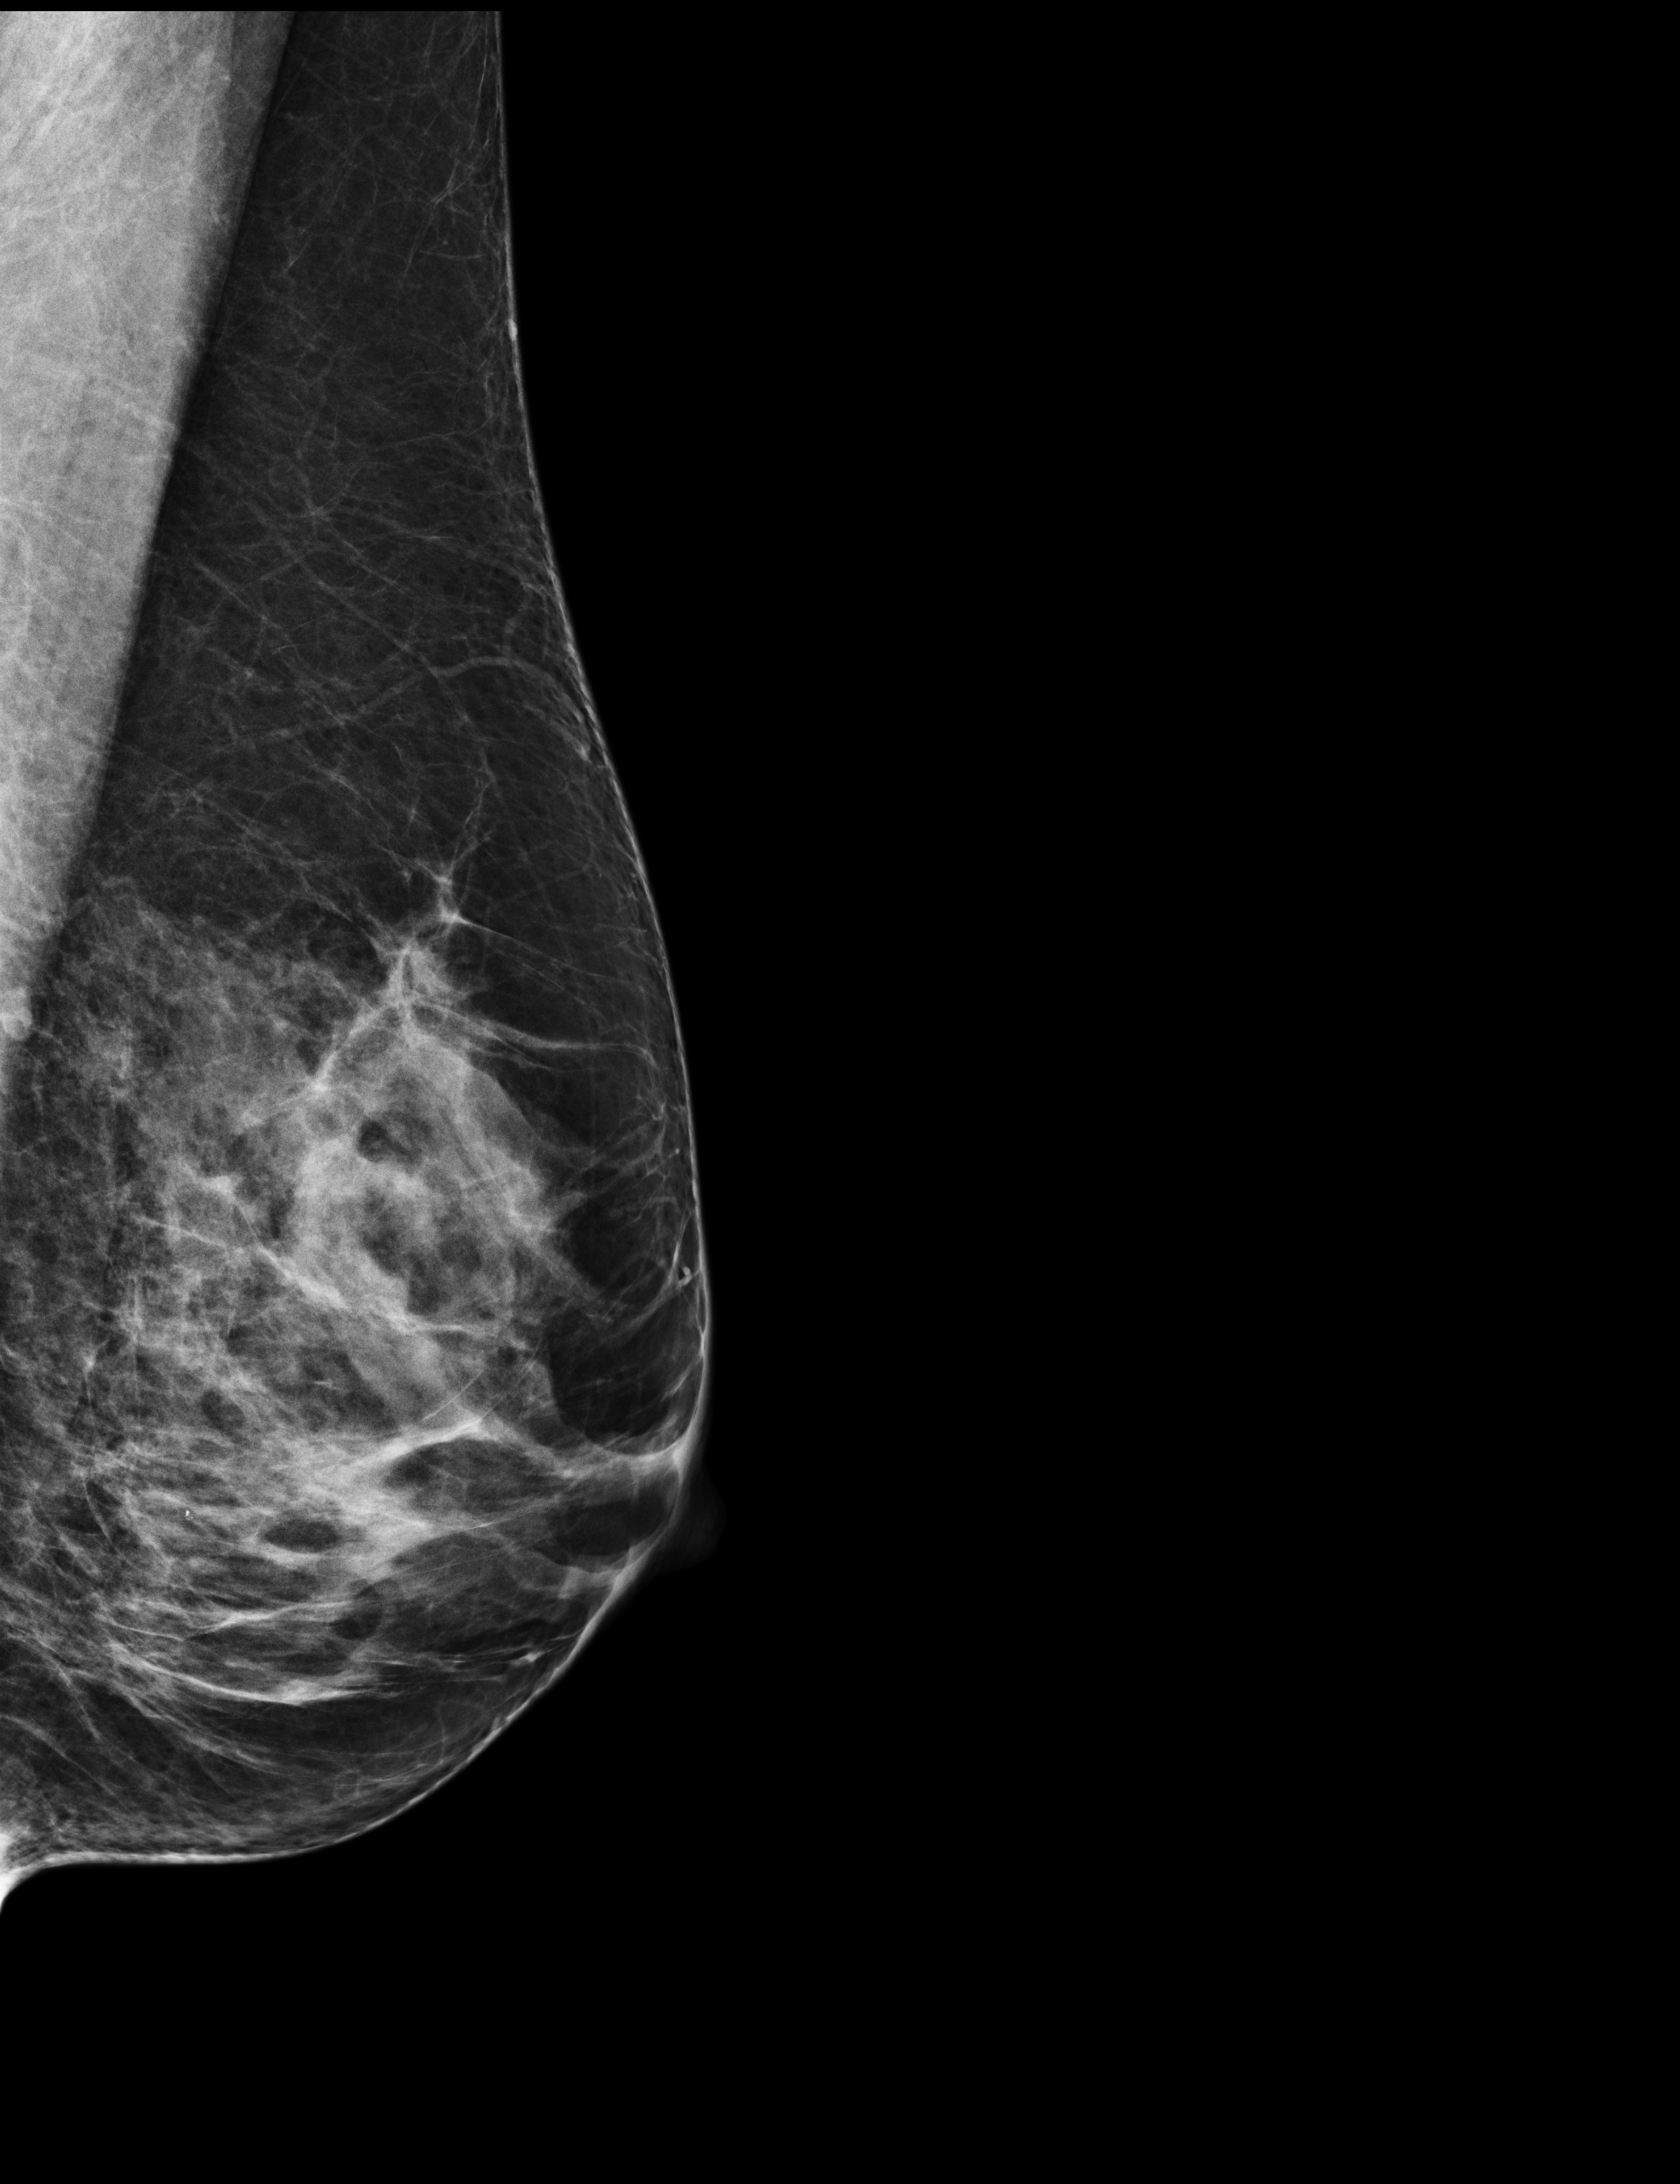
Digital mammogram (FFDM); left breast; mediolateral oblique (MLO) view; screening examination; compressed breast thickness 59 mm. Patient aged 59 years (female).
- breast density at the screening exam (both breasts): heterogeneously dense (BI-RADS density category c)
- final BI-RADS assessment for this screening round (tomosynthesis exam, both breasts): category 2
- recall: no recall after this screen